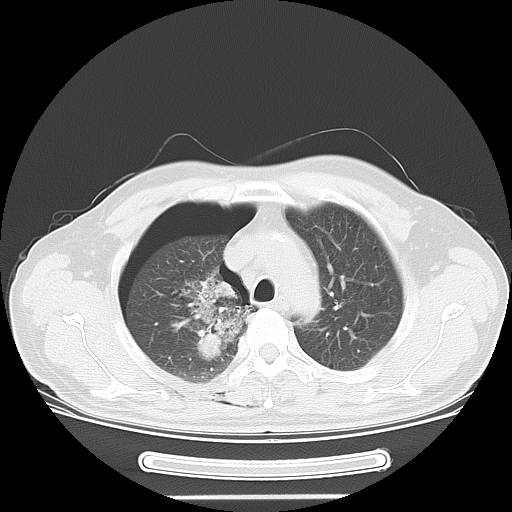
Chest CT, one axial slice; slice 44 of 57 in the series (ordered by position); reconstruction kernel LUNG; lung window (W 1500 / L -600 HU); 5 mm slice thickness; 512 × 512 image matrix, field of view 376 × 376 mm. Male patient, age 61 years. Case-level facts recorded for this patient, not image findings: clinical TNM (as recorded): T1c N3 M1b.
Annotated regions visible in this slice (bounding box drawn by a radiologist):
- lung tumour (recorded histology: adenocarcinoma): box from (x=169, y=266) to (x=257, y=364) px